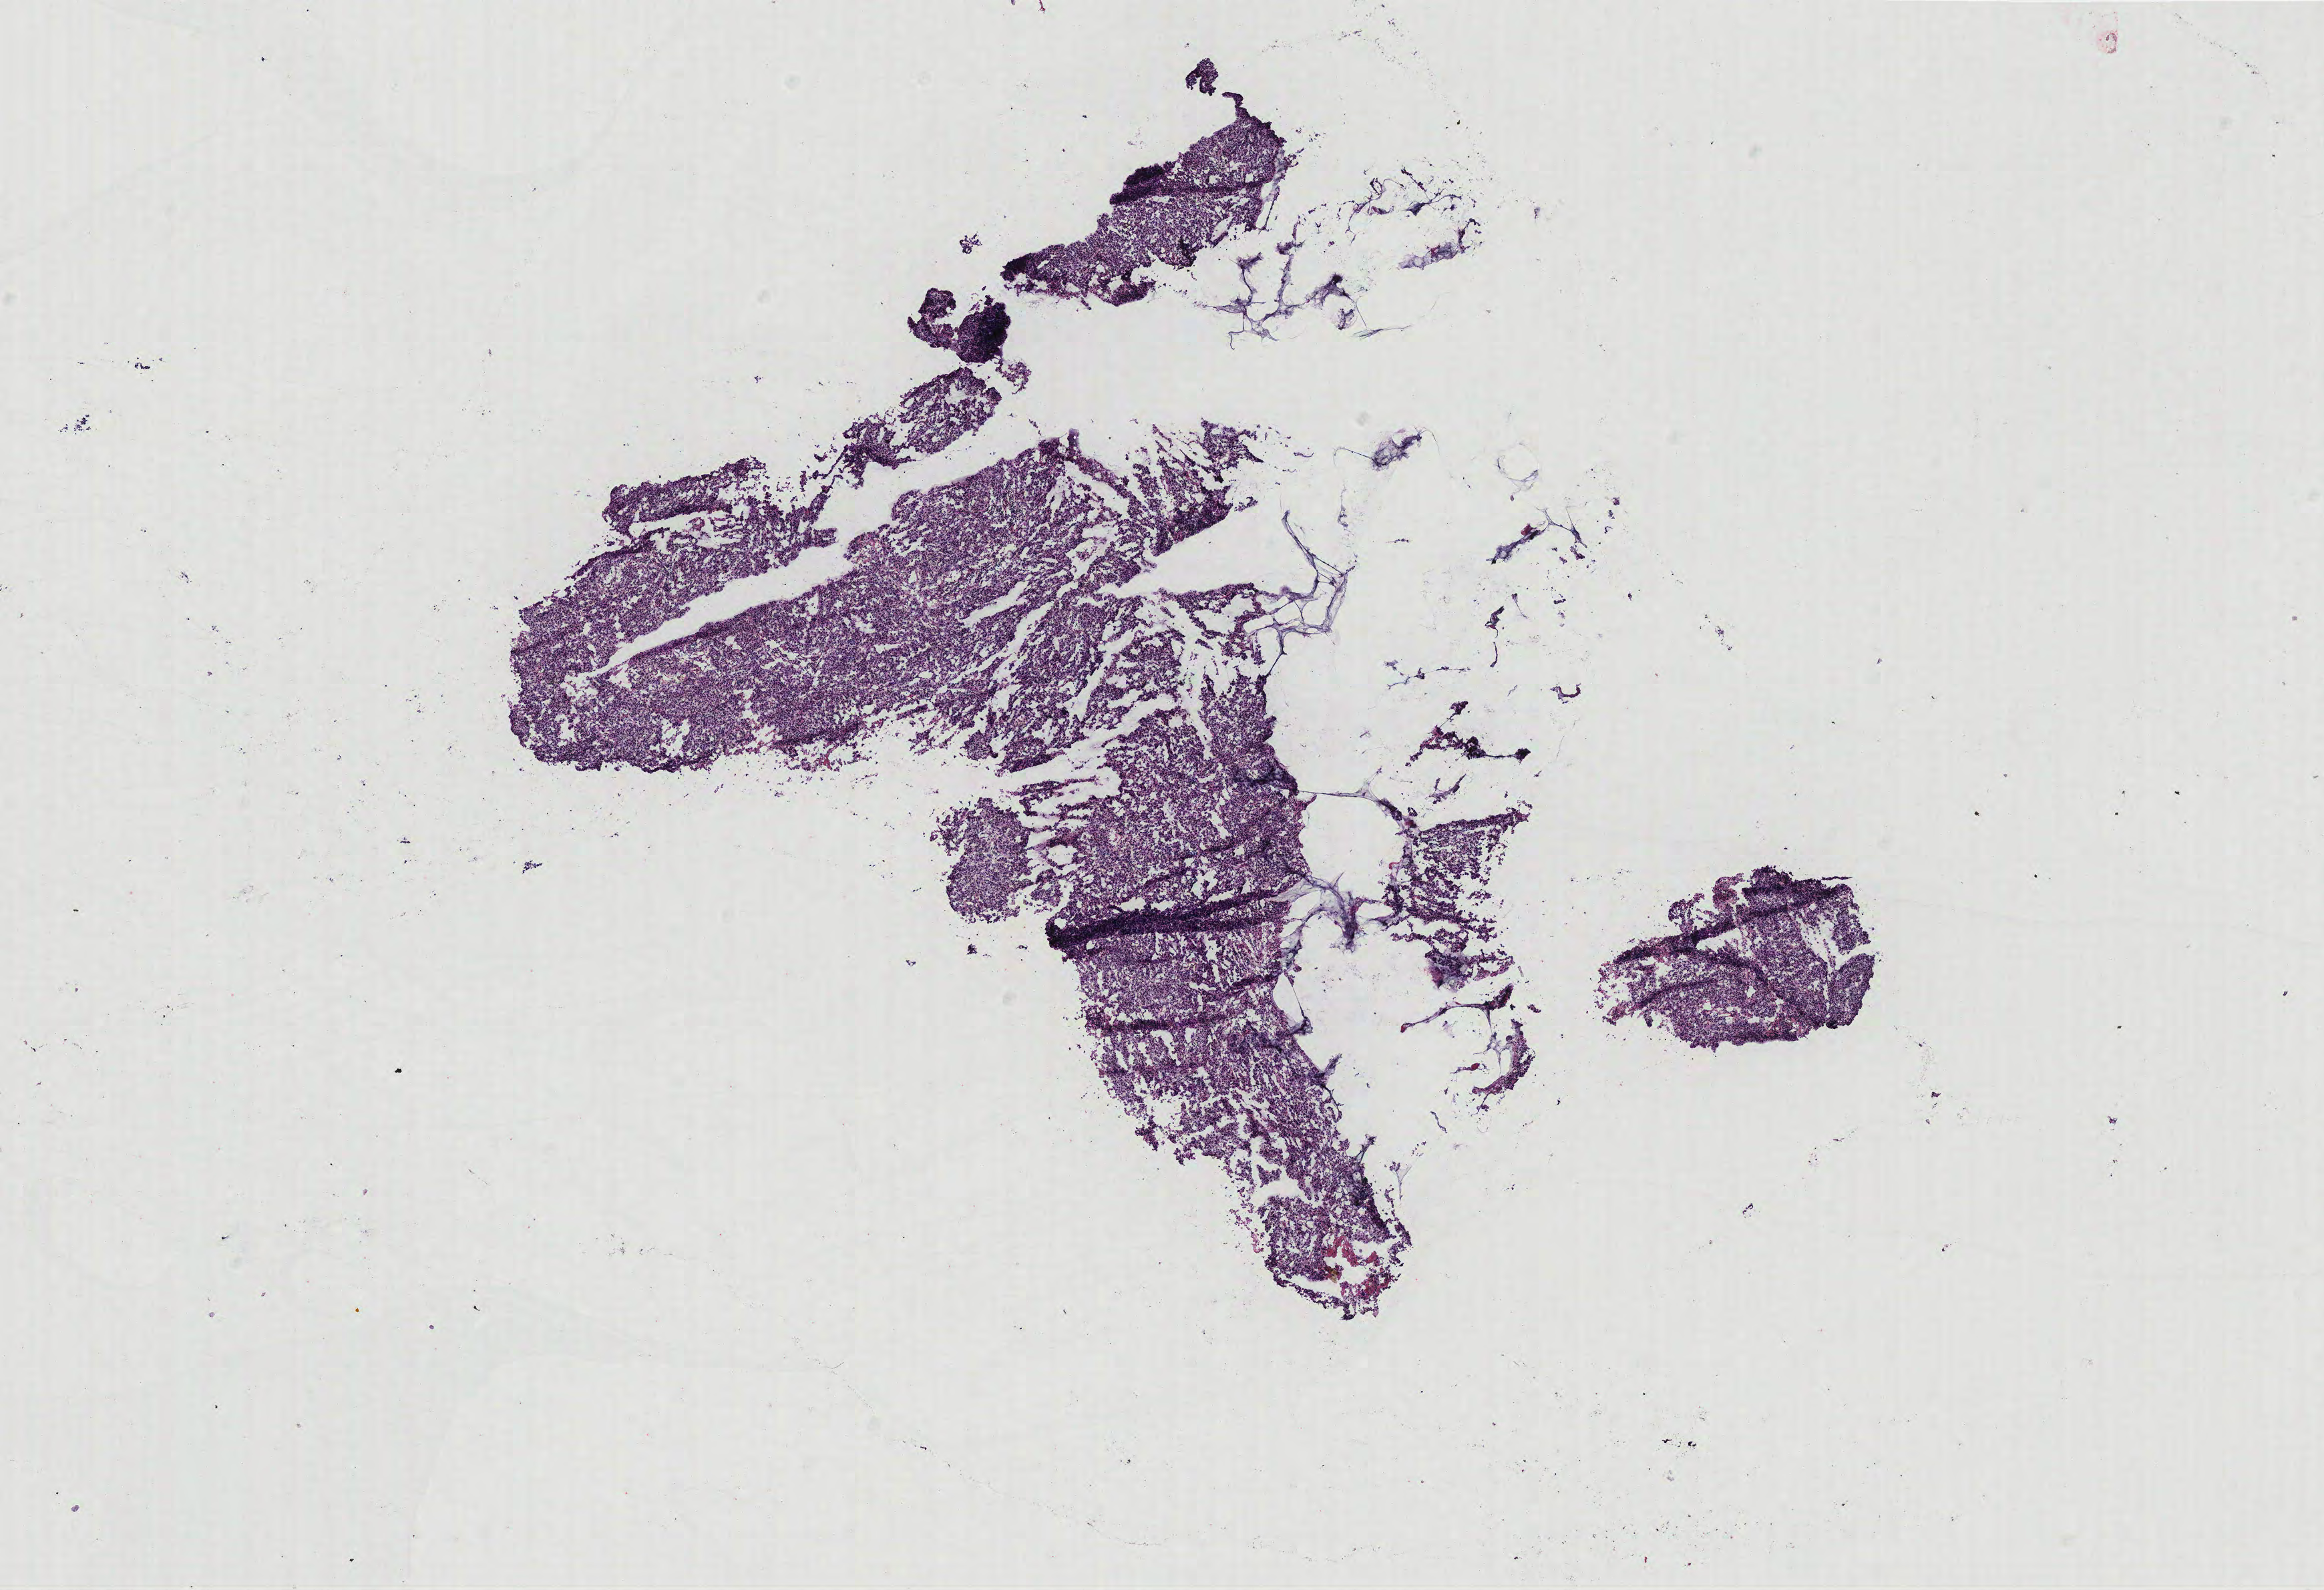
Digitized H&E-stained tissue section (whole slide), low-resolution overview of the scanned area, about 13.9 x 9.5 mm (slide scanned at 40x). Breast, tissue type not recorded. 61-year-old female patient.
* patient diagnosis: Infiltrating duct carcinoma, NOS